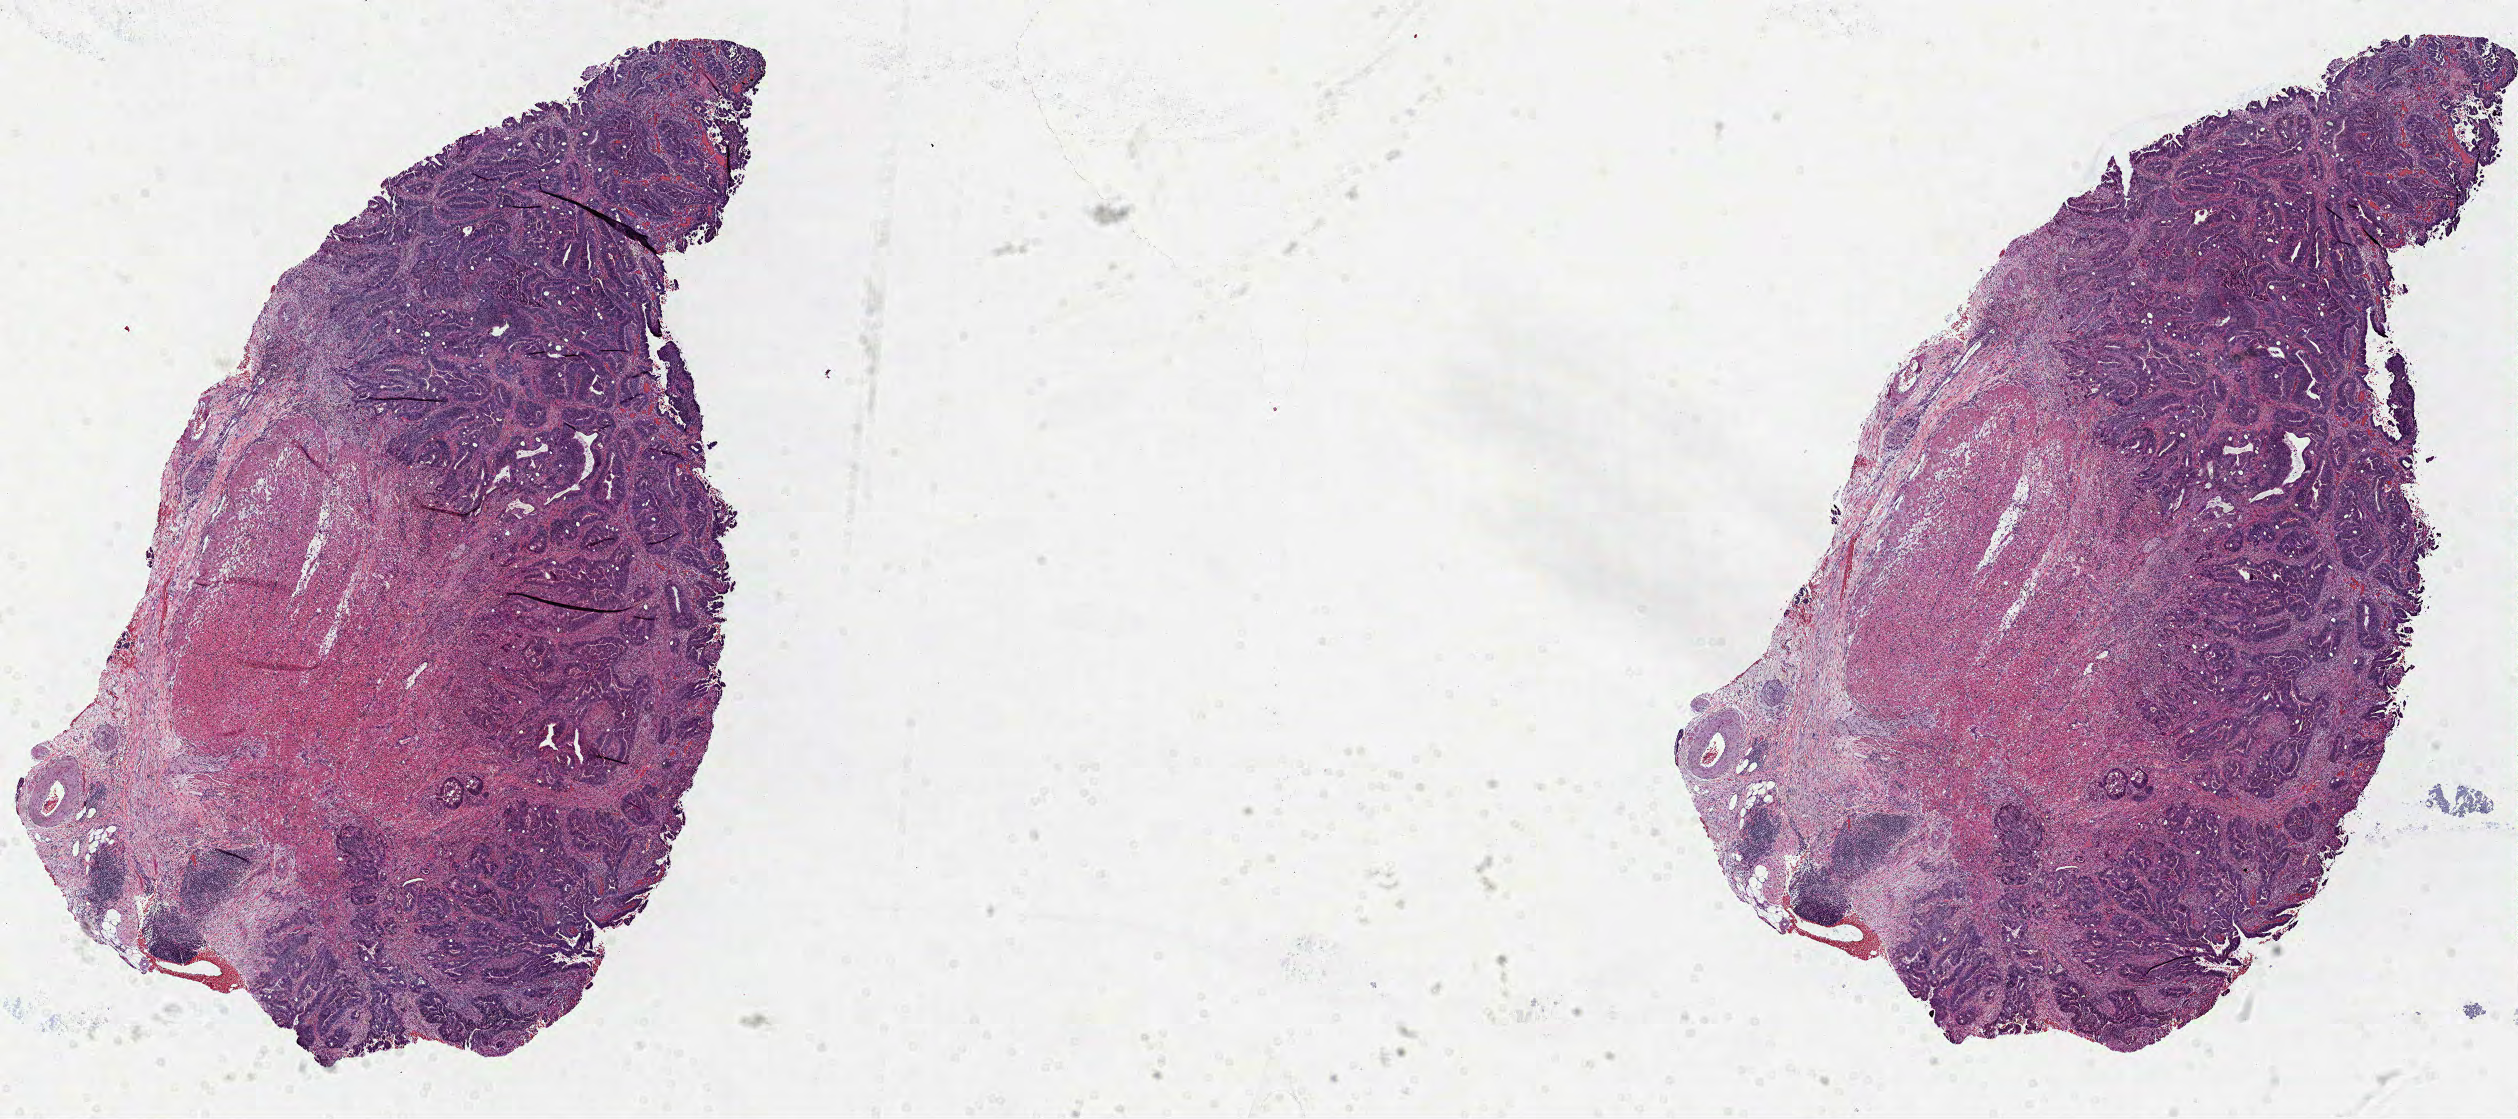
Digitized H&E tissue section (whole slide) — whole scanned area (about 20.3 x 9.0 mm, from a 40x scan) shown as a low-resolution overview; FFPE section; primary tumour sample from the colon. Male, age 65 years at initial diagnosis.
Histologic diagnosis: Adenocarcinoma, NOS. AJCC pathologic stage: IIIB.